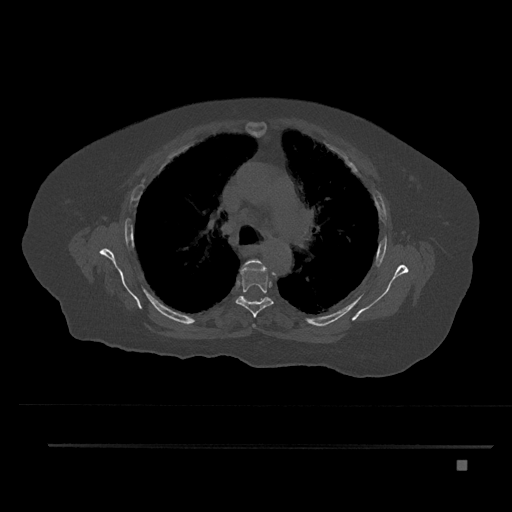
CT including the spine, one axial slice; slice 568 of 797 in the series (ordered by position); reconstruction kernel Br40s/3; 120 kVp; bone window (W 1800 / L 400 HU); 512 × 512 image matrix, field of view 437 × 437 mm. Patient: female, 76 years. From the clinical record (not read from this slice): primary cancer: lung.
Annotated regions visible in this slice (semi-automatic segmentation, software-assisted and operator-edited):
- T4 vertebra: bounding box (x1, y1, x2, y2) in pixels: (245, 259, 262, 327)
- T5 vertebra: (235, 263, 274, 318)
- T6 vertebra: (259, 299, 263, 302)